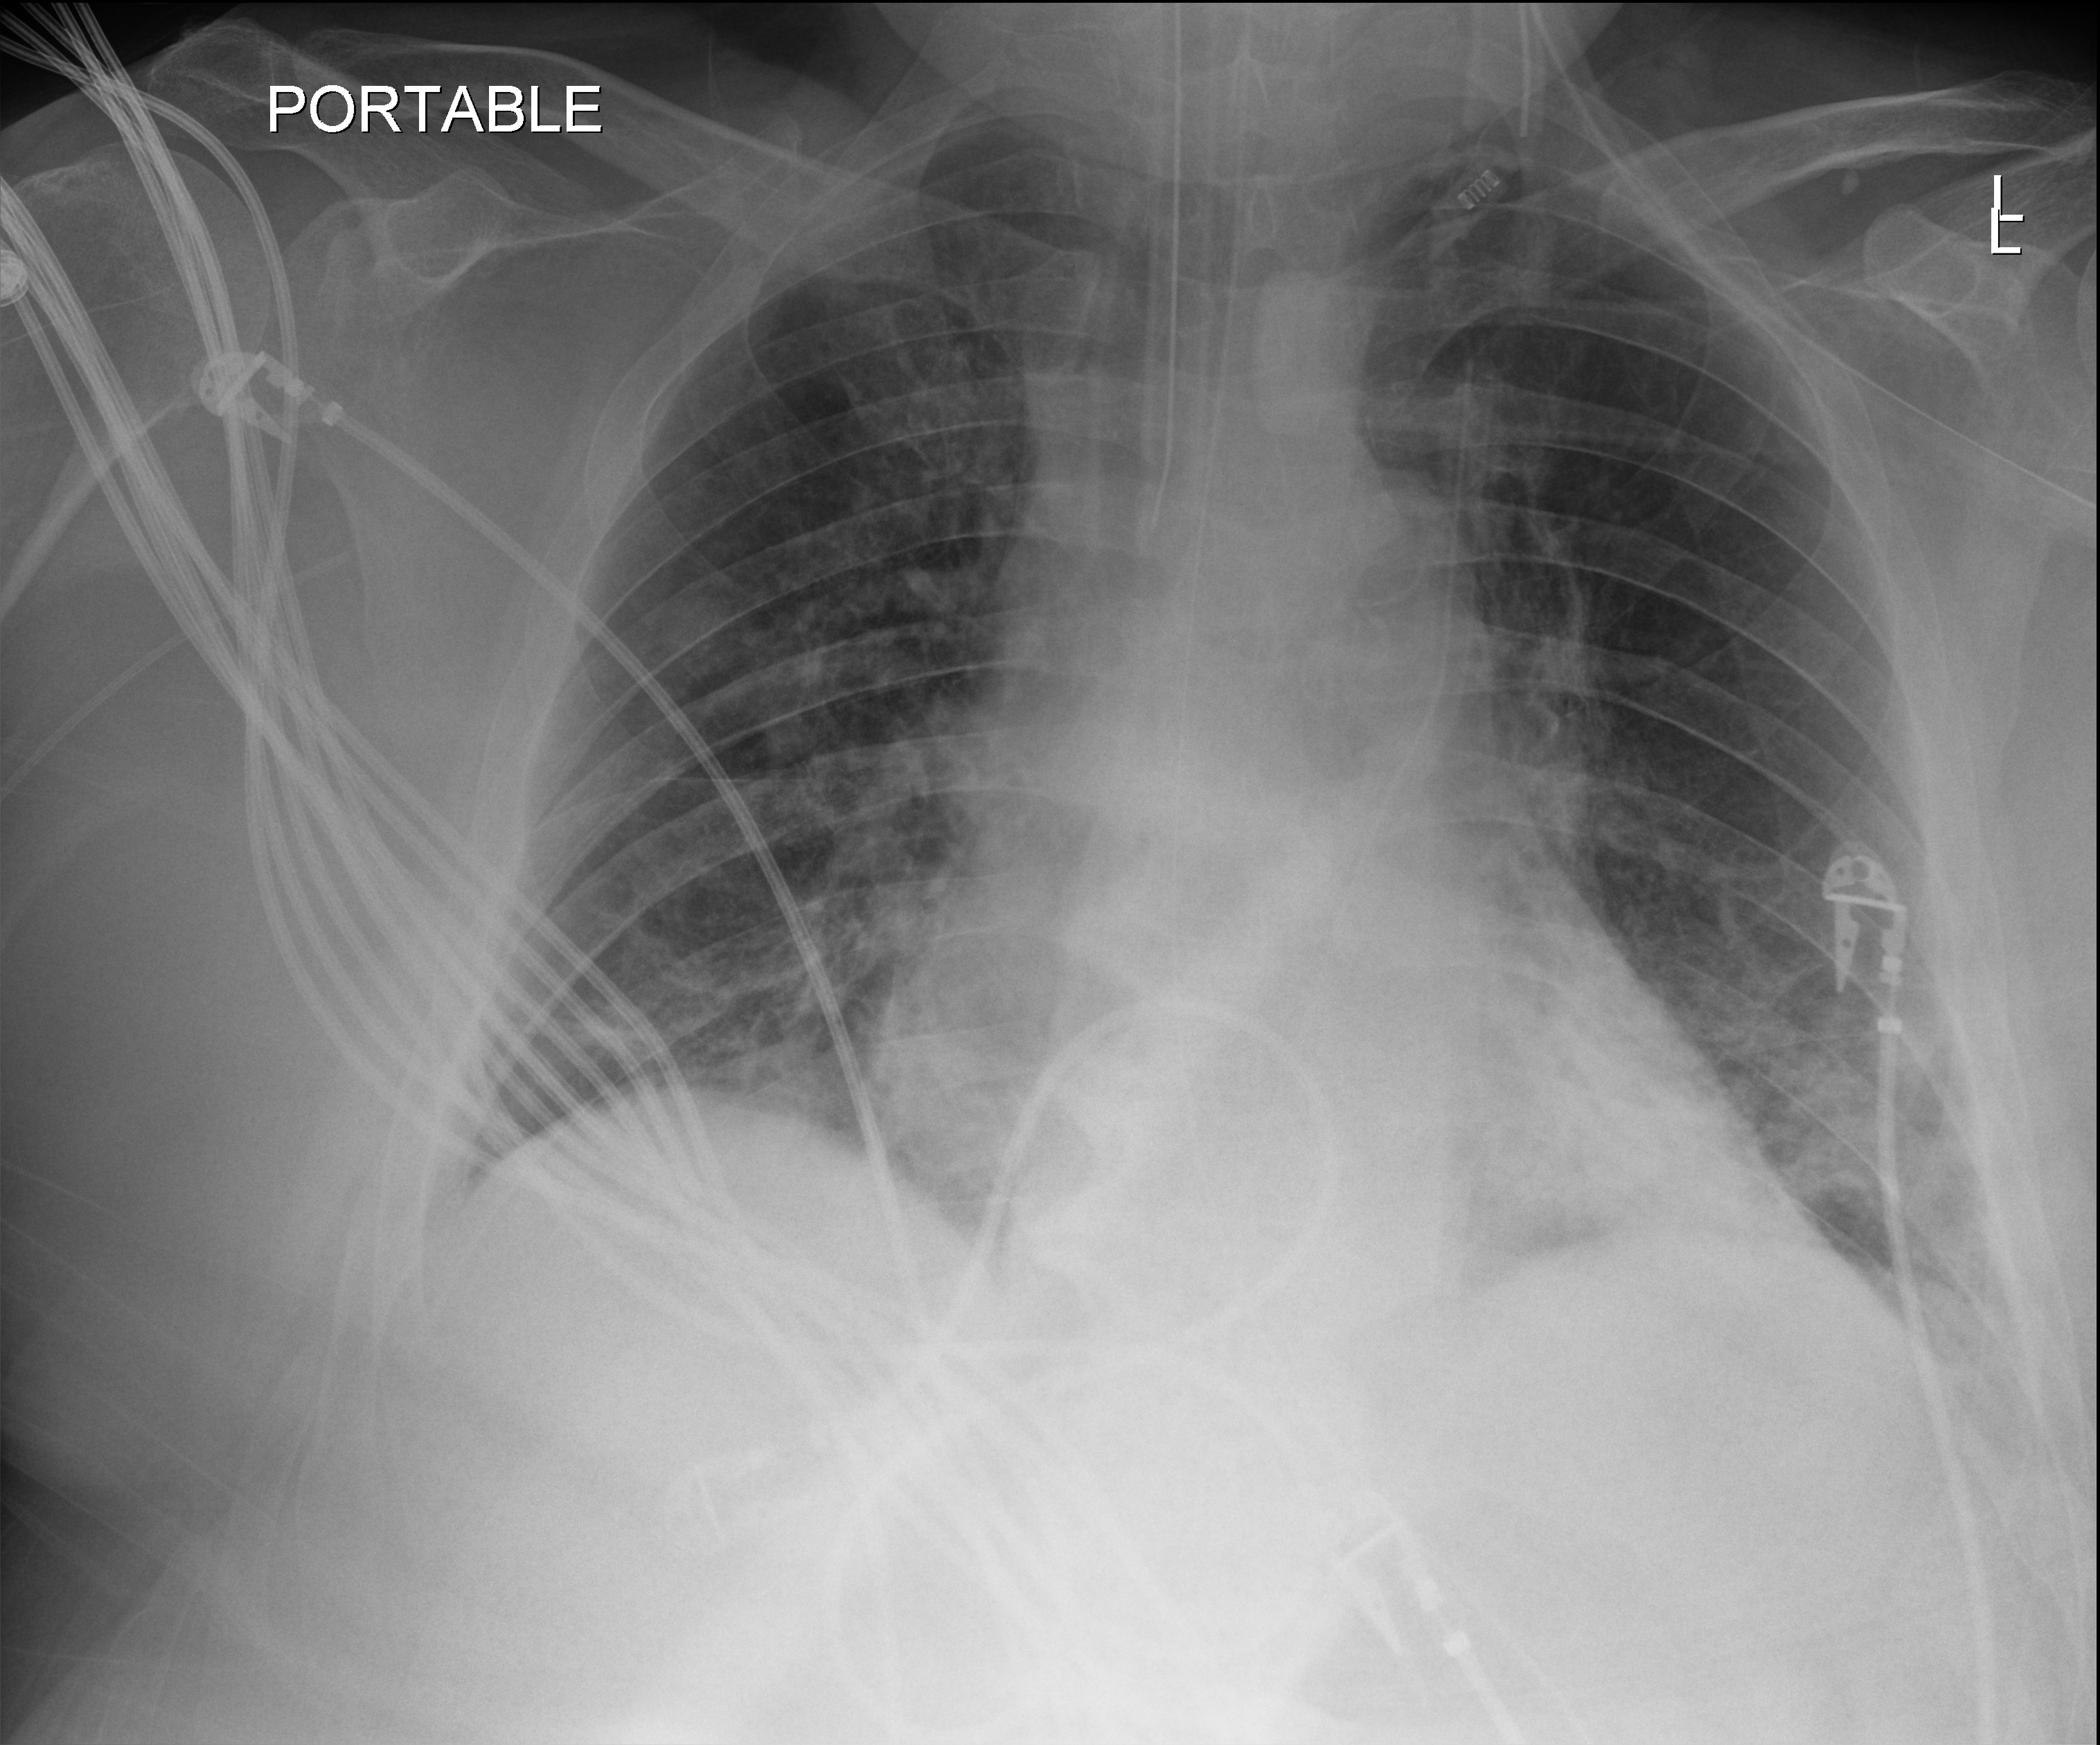
Portable chest radiograph, anteroposterior (AP) projection. Male patient hospitalised with COVID-19, age 60–74 years.
Hospital-stay facts (about this admission, not read from this image; timing relative to this image not recorded):
- diabetes (admission record): no
- mechanically ventilated during this hospital stay: yes
- admitted to intensive care during this hospital stay: yes